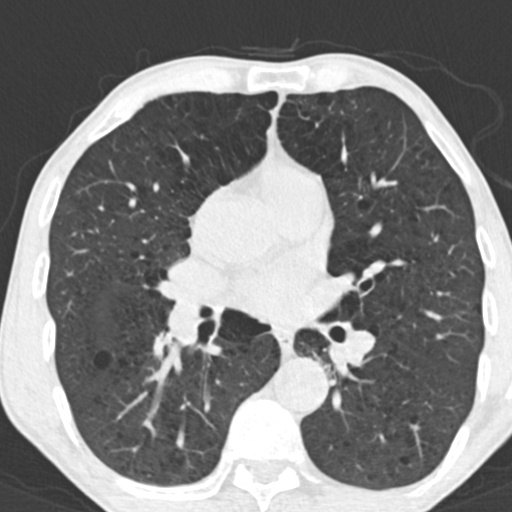
Axial slice from a low-dose chest CT screening exam, baseline annual screen, lung window (W 1500 / L -600 HU), 512 × 512 image matrix. Male participant, aged 64 years at enrolment. Current smoker at enrolment.
Expert reader's lesion annotation, box from (x=131, y=311) to (x=191, y=362) px. No non-calcified nodule or mass ≥4 mm was recorded by the screening reader at this exam. Participant outcome: lung cancer diagnosed 386 days after this screen — adenocarcinoma, NOS, right lower lobe, stage IV (AJCC 6th edition), 60 mm at pathology.